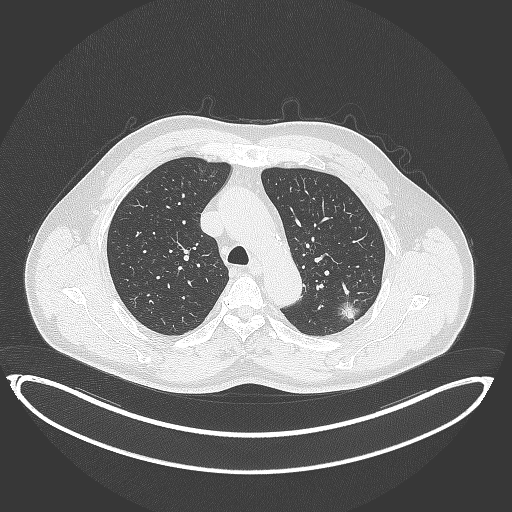
Chest CT, one axial slice; slice 264 of 399 in the series (ordered by position); lung window (W 1500 / L -600 HU); 512 × 512 image matrix. Male patient, age 58 years. From the clinical record (not read from this slice): clinical TNM (as recorded): T1c N0 M0; histopathological grade: G1-2.
Structures marked on this image (bounding box drawn by a radiologist):
- lung tumour (recorded histology: adenocarcinoma): box from (x=337, y=295) to (x=365, y=325) px